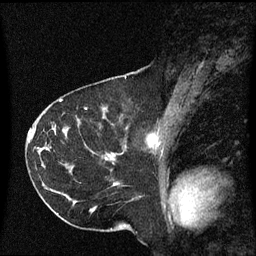
Breast MRI (dynamic contrast-enhanced), one sagittal slice. Slice 36 of 60 in the series (ordered by position). Dynamic contrast-enhanced series, image 2 of 3 at this slice position (ordered by acquisition). 1.5 T. TE 4.2 ms, TR 8.4 ms. 2 mm slice thickness. 256 × 256 image matrix, field of view 220 × 220 mm. Female patient, age 41 years. From the clinical record (not read from this slice): setting: breast cancer imaged before/during neoadjuvant chemotherapy; receptor status: triple-negative.
Structures marked on this image (semi-automatic segmentation, software-assisted and operator-edited):
- analysis volume of interest (the breast-tissue region the enhancement analysis was run in; not a lesion): bounding box (x1, y1, x2, y2) in pixels: (116, 136, 156, 155)
- tumour enhancement mask (voxels above the 70 % enhancement threshold inside the analysis volume of interest): (151, 136, 156, 143)